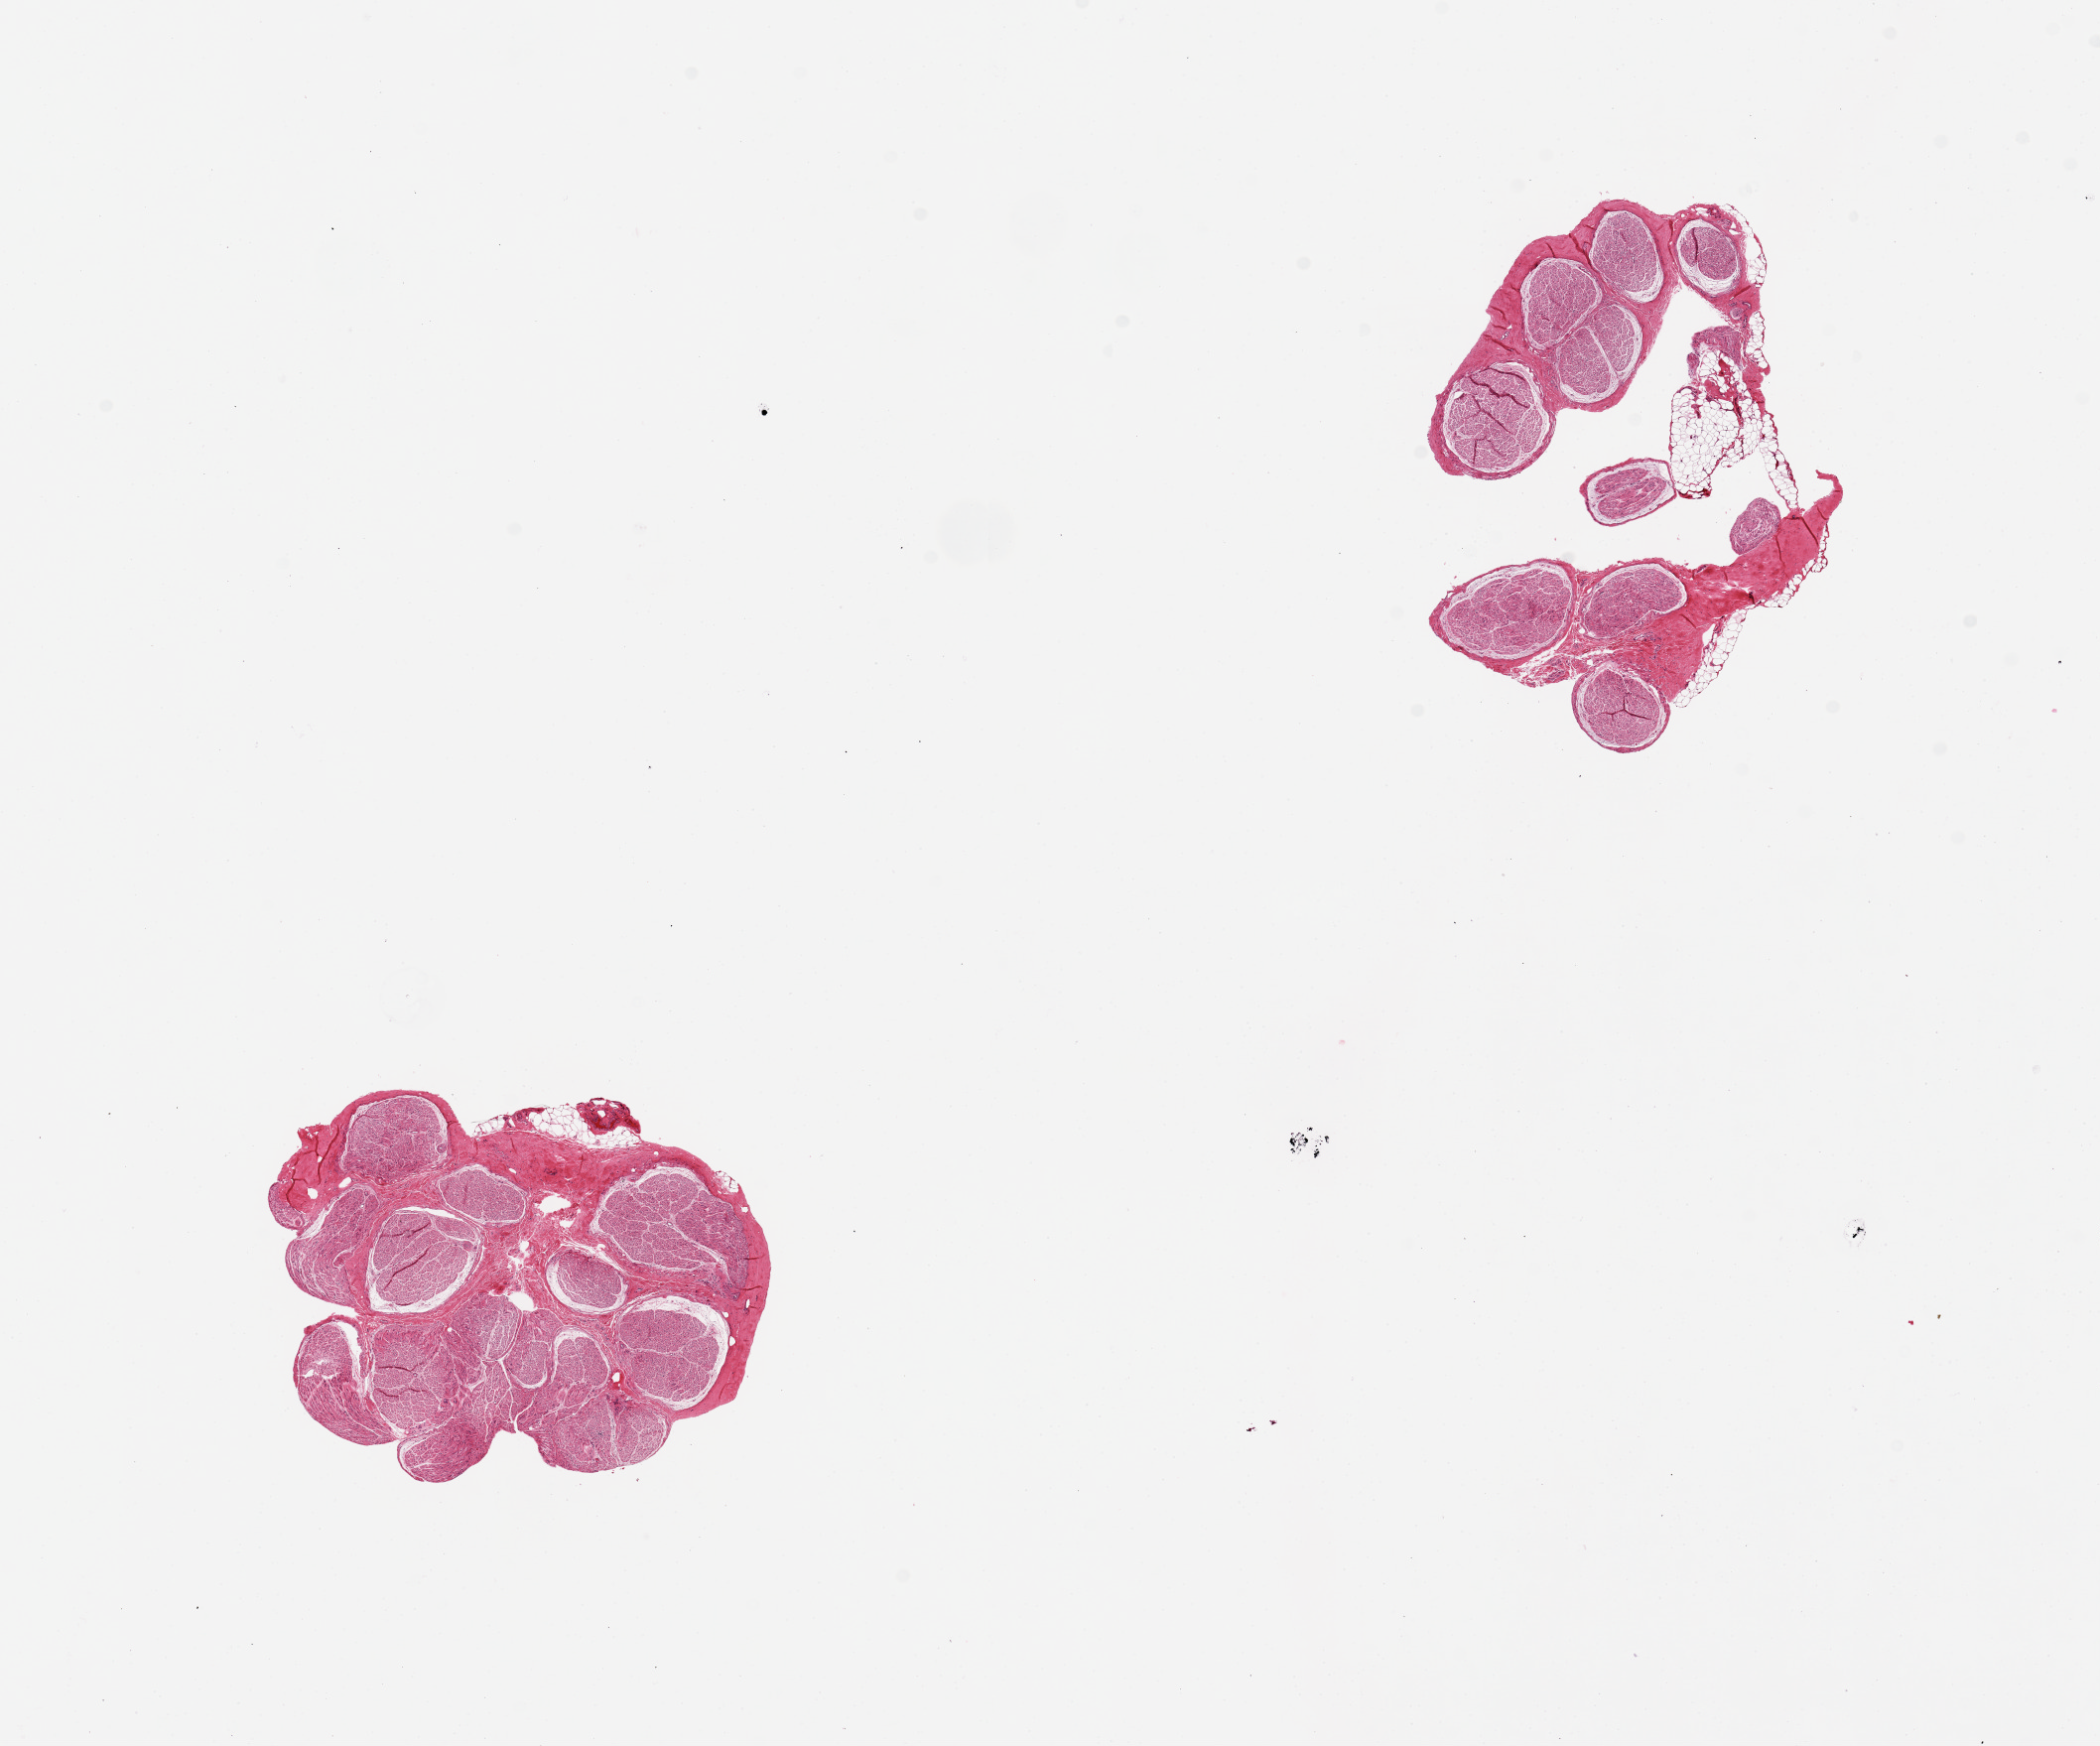
Whole-slide image, haematoxylin and eosin stain, a low-resolution overview of the entire scanned area, about 16.7 x 13.9 mm (acquisition: 20x scan). PAXgene-fixed, paraffin-embedded tissue. Sampled site (target tissue): tibial nerve. Tissue donor sample. Donor sex: male.
* review note (as recorded): 2 pieces 4 x 3 and 4 x 3 mm. One piece with 10% adipose